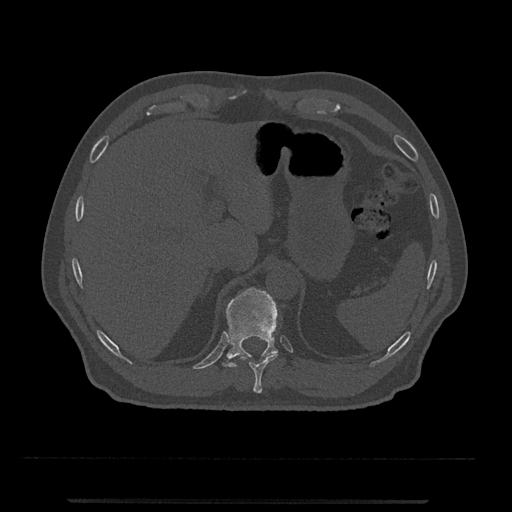
CT including the spine, one axial slice; reconstruction kernel Br40s/3; bone window (W 1800 / L 400 HU); 0.5 mm slice thickness; 512 × 512 image matrix, field of view 419 × 419 mm. Patient: male, 63 years. Case-level facts recorded for this patient, not image findings: primary cancer: prostate.
Structures marked on this image (semi-automatic segmentation, software-assisted and operator-edited):
- T10 vertebra: box from (x=241, y=353) to (x=278, y=393) px
- T11 vertebra: (x=223, y=287)–(x=278, y=368)